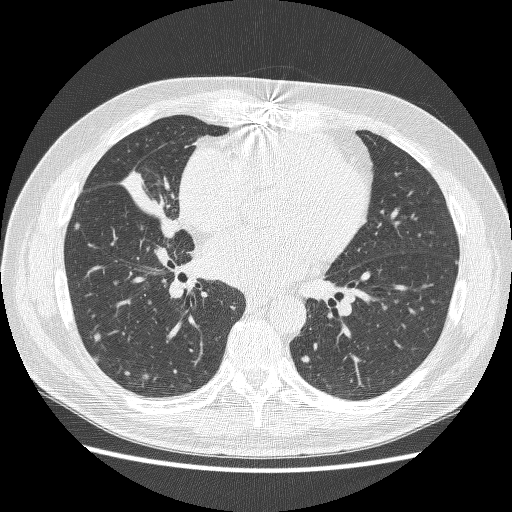
Chest CT (low-dose screening protocol), one axial image. First (baseline) screen. Lung window (W 1500 / L -600 HU). 1.25 mm slice thickness. Lung (sharp) reconstruction kernel (BONE). Male participant, aged 59 years at enrolment. Former smoker at enrolment.
Expert-annotated lung lesion, bounding box <111,160,196,247> (left, top, right, bottom; pixels). Screening reader's record for this exam: no non-calcified nodule ≥4 mm recorded.